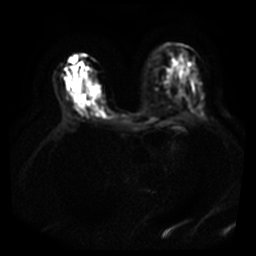
Breast MRI, one axial slice; slice 23 of 40 in the series (ordered by position); diffusion-weighted series; image 2 of 4 stored at this slice position (different b-values; order by instance number); 3 T; 5 mm slice thickness; 256 × 256 image matrix, field of view 380 × 380 mm. Female patient.
Structures marked on this image (expert manual segmentation):
- tumour on diffusion-weighted imaging: box from (x=89, y=86) to (x=93, y=91) px